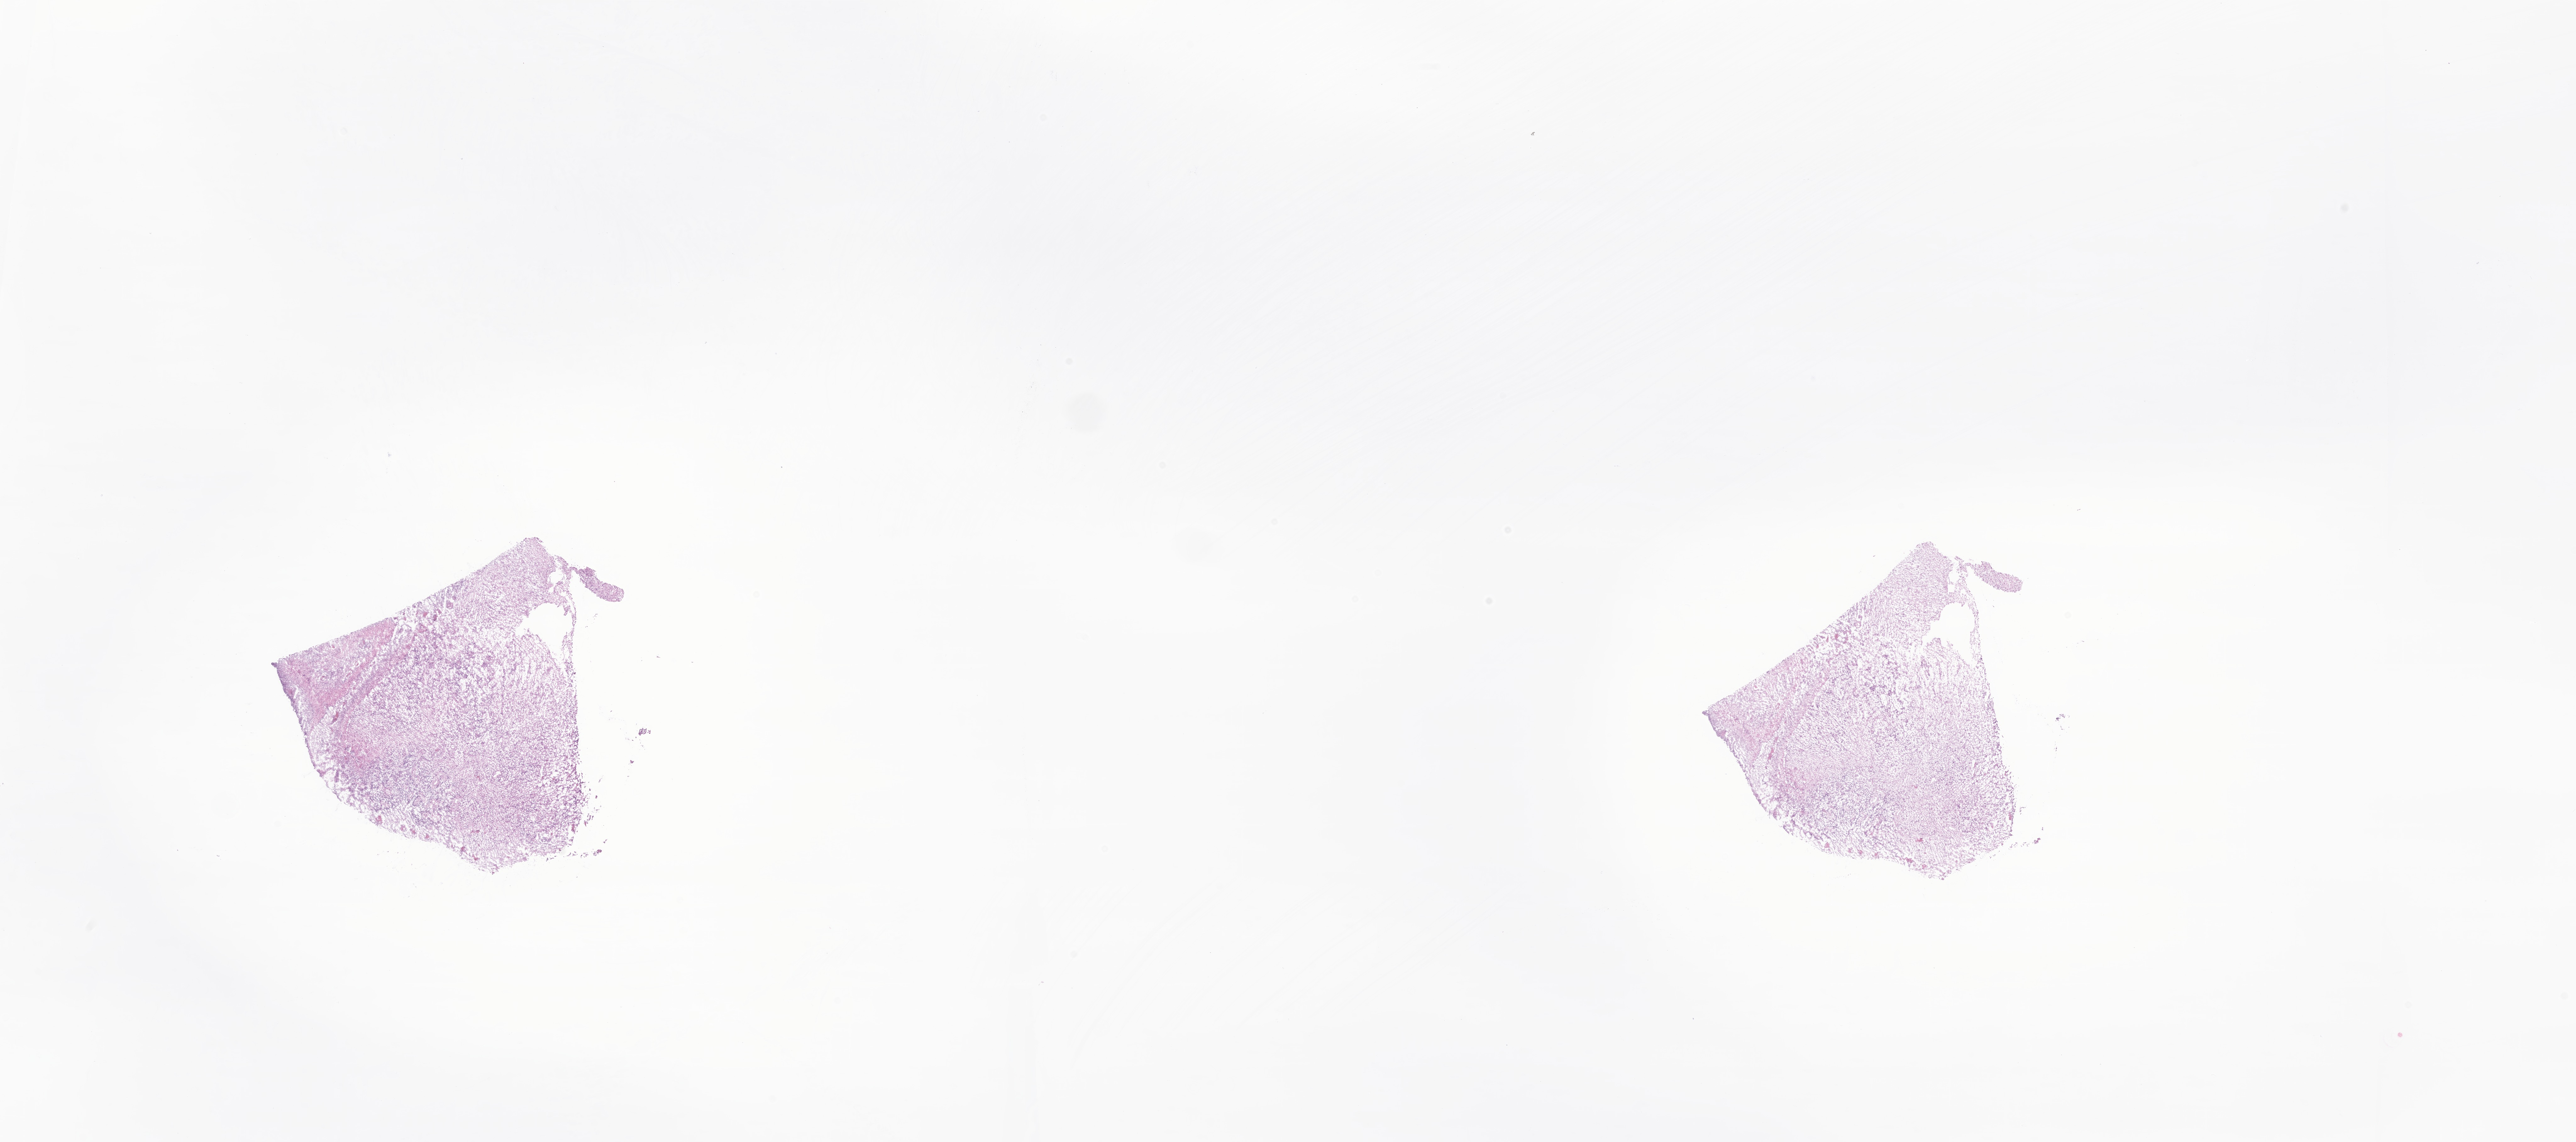
H&E whole-slide image of tumor tissue from the brain — shown as a low-resolution overview of the whole scanned area (about 34.5 x 15.3 mm), cryosection (OCT / tissue freezing medium). Male patient, age 34 months (2 years 10 months).
Diagnosis (ICD-O-3 morphology term): Ependymoma, NOS.